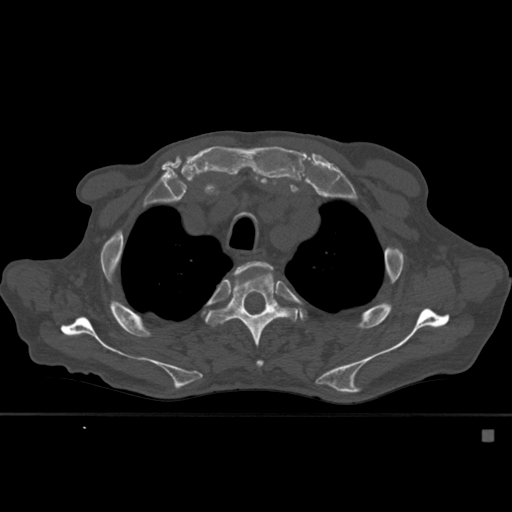
CT including the spine, one axial slice; position 419 of 527 along the scan axis; bone window (W 1800 / L 400 HU); 1.5 mm slice thickness; 512 × 512 image matrix, field of view 373 × 373 mm. Male patient, age 78 years. Case-level facts recorded for this patient, not image findings: primary cancer: prostate.
Annotated regions visible in this slice (semi-automatically segmented with operator editing):
- T3 vertebra: bounding box [x1, y1, x2, y2] px = [234, 261, 273, 280]
- T4 vertebra: [205, 268, 299, 368]